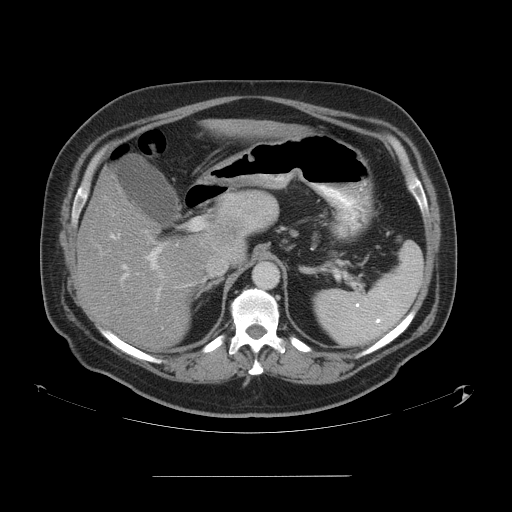
Contrast-enhanced abdominal CT, one axial slice; slice 34 of 58 in the series (ordered by position); 120 kVp; soft-tissue window (W 400 / L 40 HU); 5 mm slice thickness; 512 × 512 image matrix, field of view 480 × 480 mm. Male patient, age 63 years. Case-level facts recorded for this patient, not image findings: diagnosis: colorectal cancer liver metastases, imaged before liver resection; multiple liver metastases: no; largest metastasis: 4.2 cm; disease in both lobes: no.
Outlined on this slice (manually delineated by an expert):
- liver: bounding box [x1, y1, x2, y2] px = [77, 122, 286, 347]
- planned liver remnant (the part of the liver to remain after resection): [77, 191, 205, 347]
- portal vein (with intrahepatic branches): [111, 219, 204, 329]
- liver metastasis: [217, 225, 243, 240]